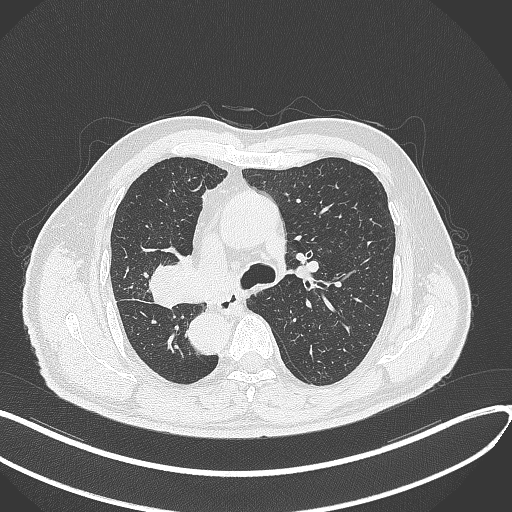
Chest CT, one axial slice. Position 198 of 300 along the scan axis. 120 kVp. Lung window (W 1500 / L -600 HU). 1 mm slice thickness. 512 × 512 image matrix, field of view 400 × 400 mm. Patient: male, 67 years. From the clinical record (not read from this slice): clinical TNM (as recorded): T2a N0 M0.
Outlined on this slice (rectangle marked by the reading radiologist):
- lung tumour (recorded histology: squamous cell carcinoma): bounding box [x1, y1, x2, y2] px = [142, 257, 195, 312]